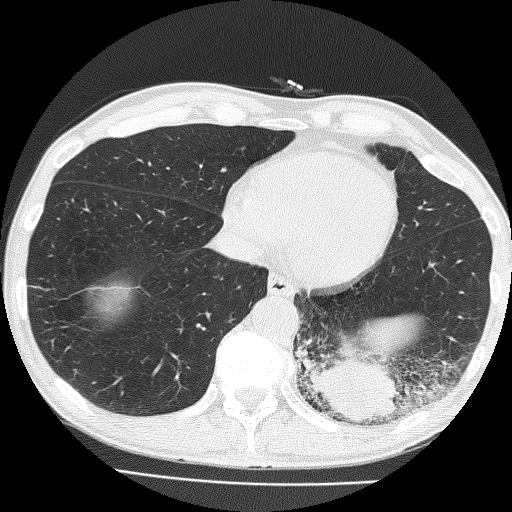
Axial slice from a low-dose chest CT screening exam, baseline annual screen, lung window (W 1500 / L -600 HU), 2 mm slice thickness, slice 110 of 160 in the series, 512 × 512 image matrix, field of view 324 × 324 mm. Male, age 58 years at enrolment. Current smoker at enrolment.
• Lesion marked by an expert reader, bounding box (x1, y1, x2, y2) in pixels: (289, 293, 430, 435).
• The screening reader recorded 2 non-calcified nodules or masses ≥4 mm on this exam; which of them this box marks is not recorded.
• Later outcome: lung cancer diagnosed 39 days after this screen — non-small cell carcinoma, left lower lobe, poorly differentiated (G3), stage IV (AJCC 6th edition), 74 mm at pathology.